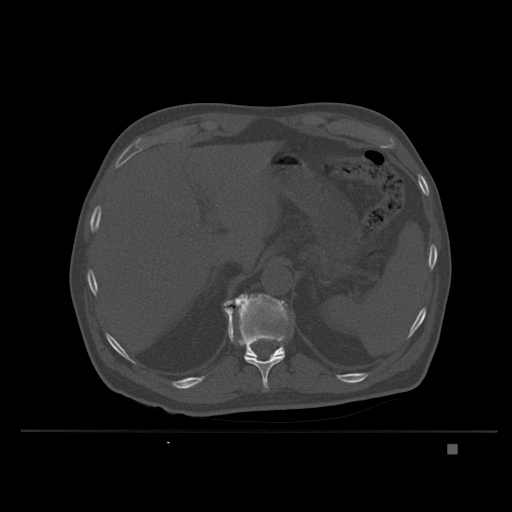
CT including the spine, one axial slice; position 170 of 435 along the scan axis; bone window (W 1800 / L 400 HU); 512 × 512 image matrix, field of view 434 × 434 mm. Male patient, age 73 years. From the clinical record (not read from this slice): primary cancer: skin.
Annotated regions visible in this slice (semi-automatically segmented with operator editing):
- T11 vertebra: bounding box [x1, y1, x2, y2] px = [226, 310, 285, 392]
- T12 vertebra: [223, 294, 289, 358]